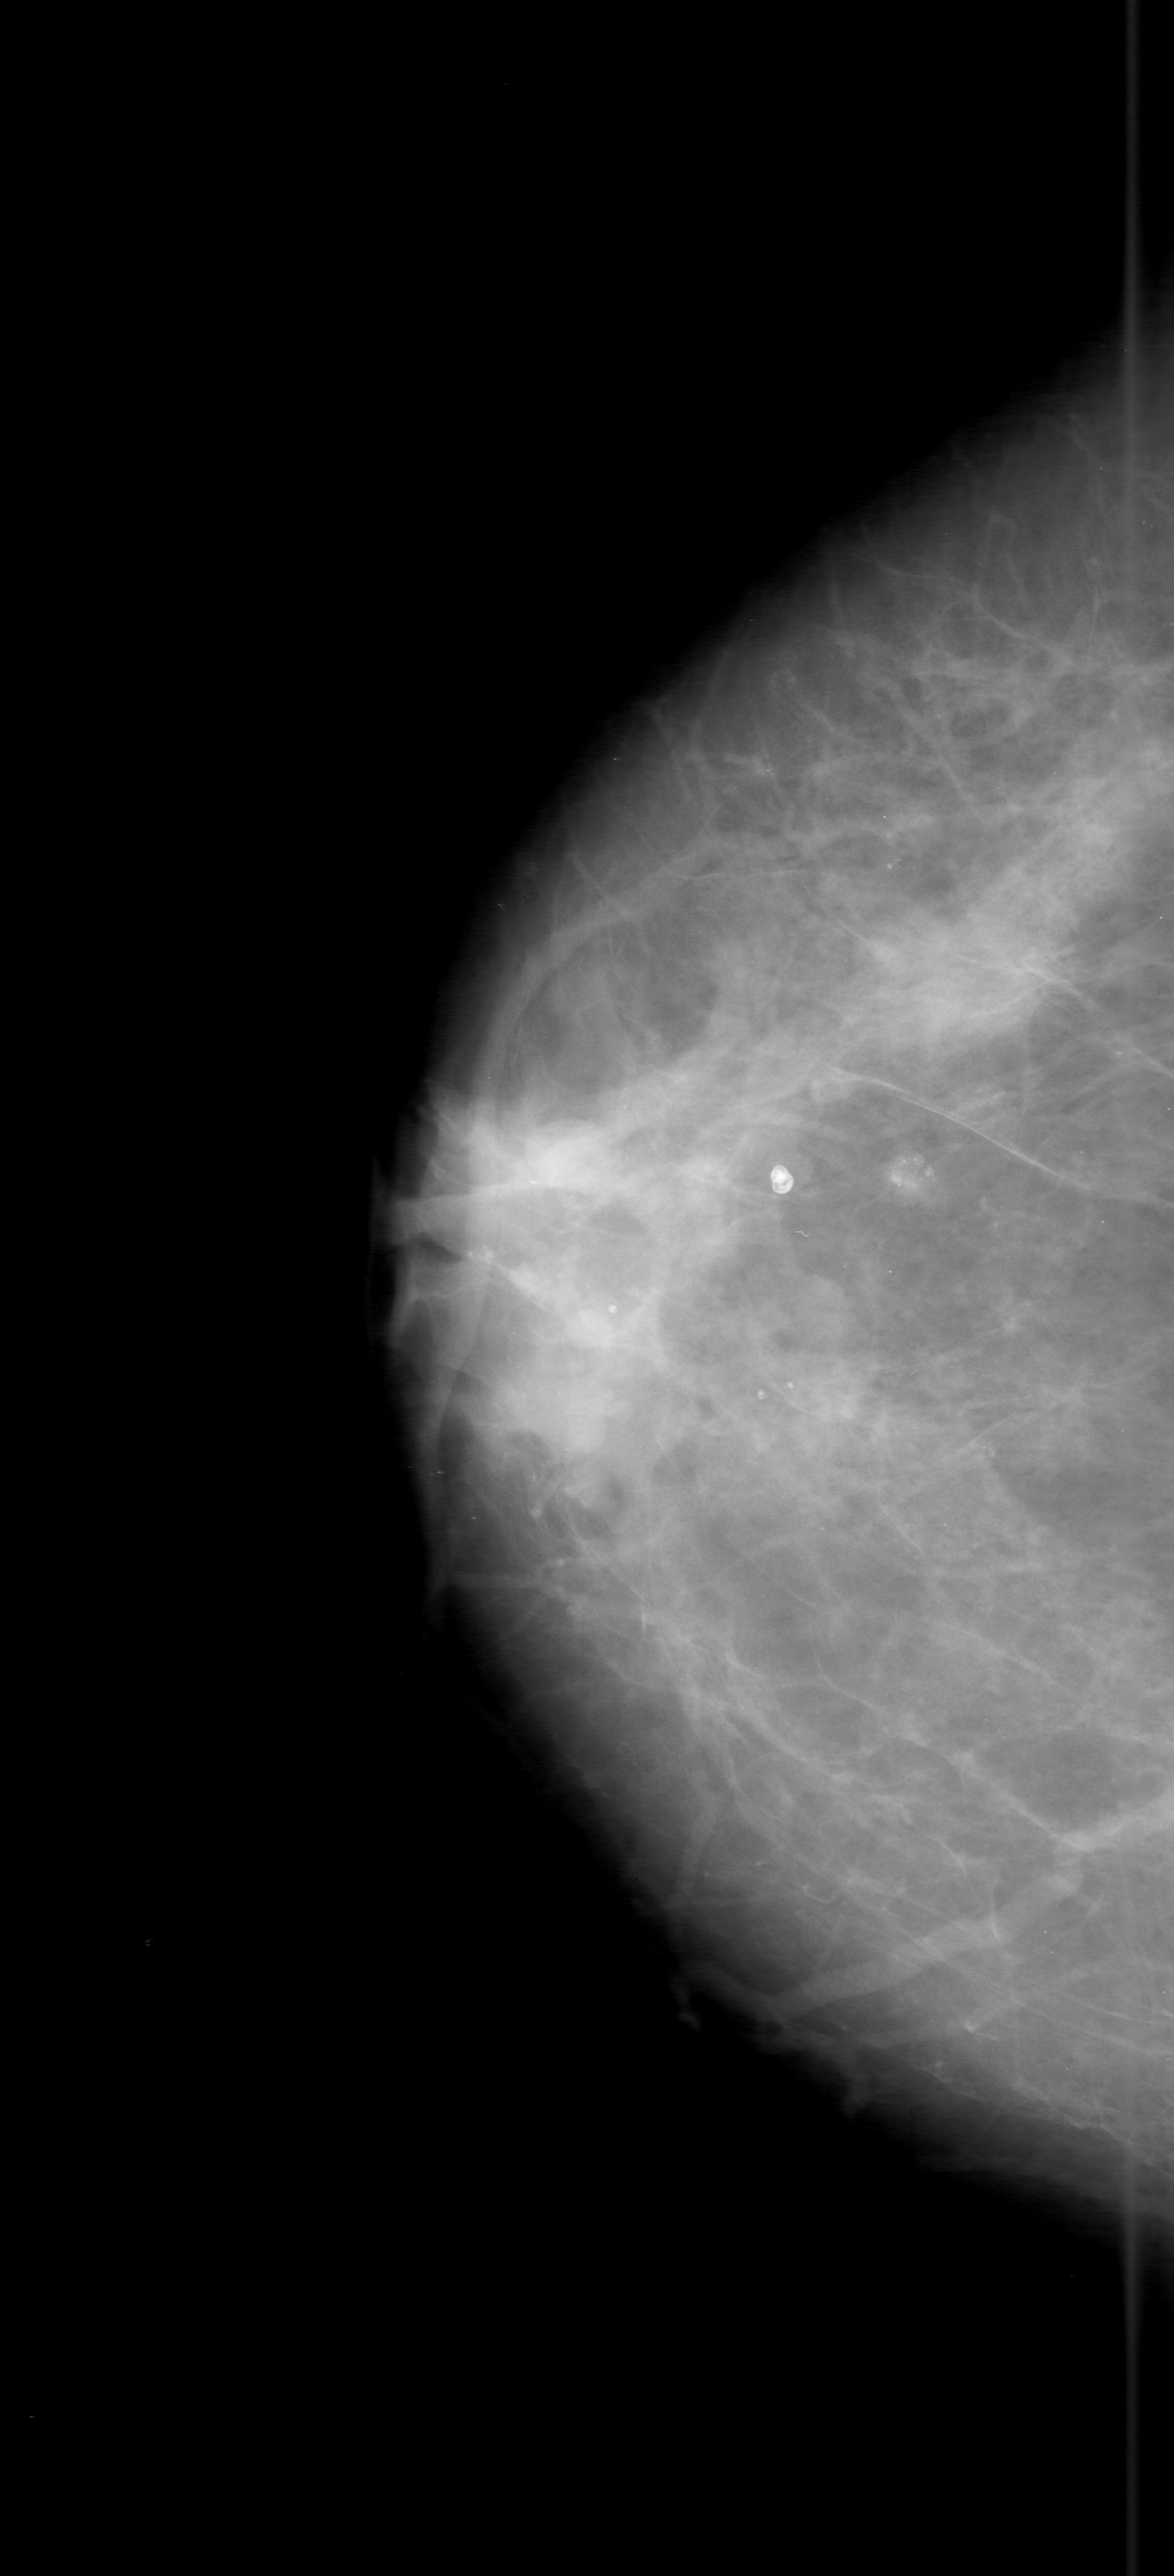
Scanned film-screen mammogram, right breast, craniocaudal (CC) view, BI-RADS breast density category 2 (scale 1–4).
Marked abnormality: calcifications, morphology amorphous, distribution clustered; BI-RADS assessment category 3; subtlety rating 3 on a 1 (subtle) to 5 (obvious) scale; pathology result (as recorded, not read from the image): malignant.